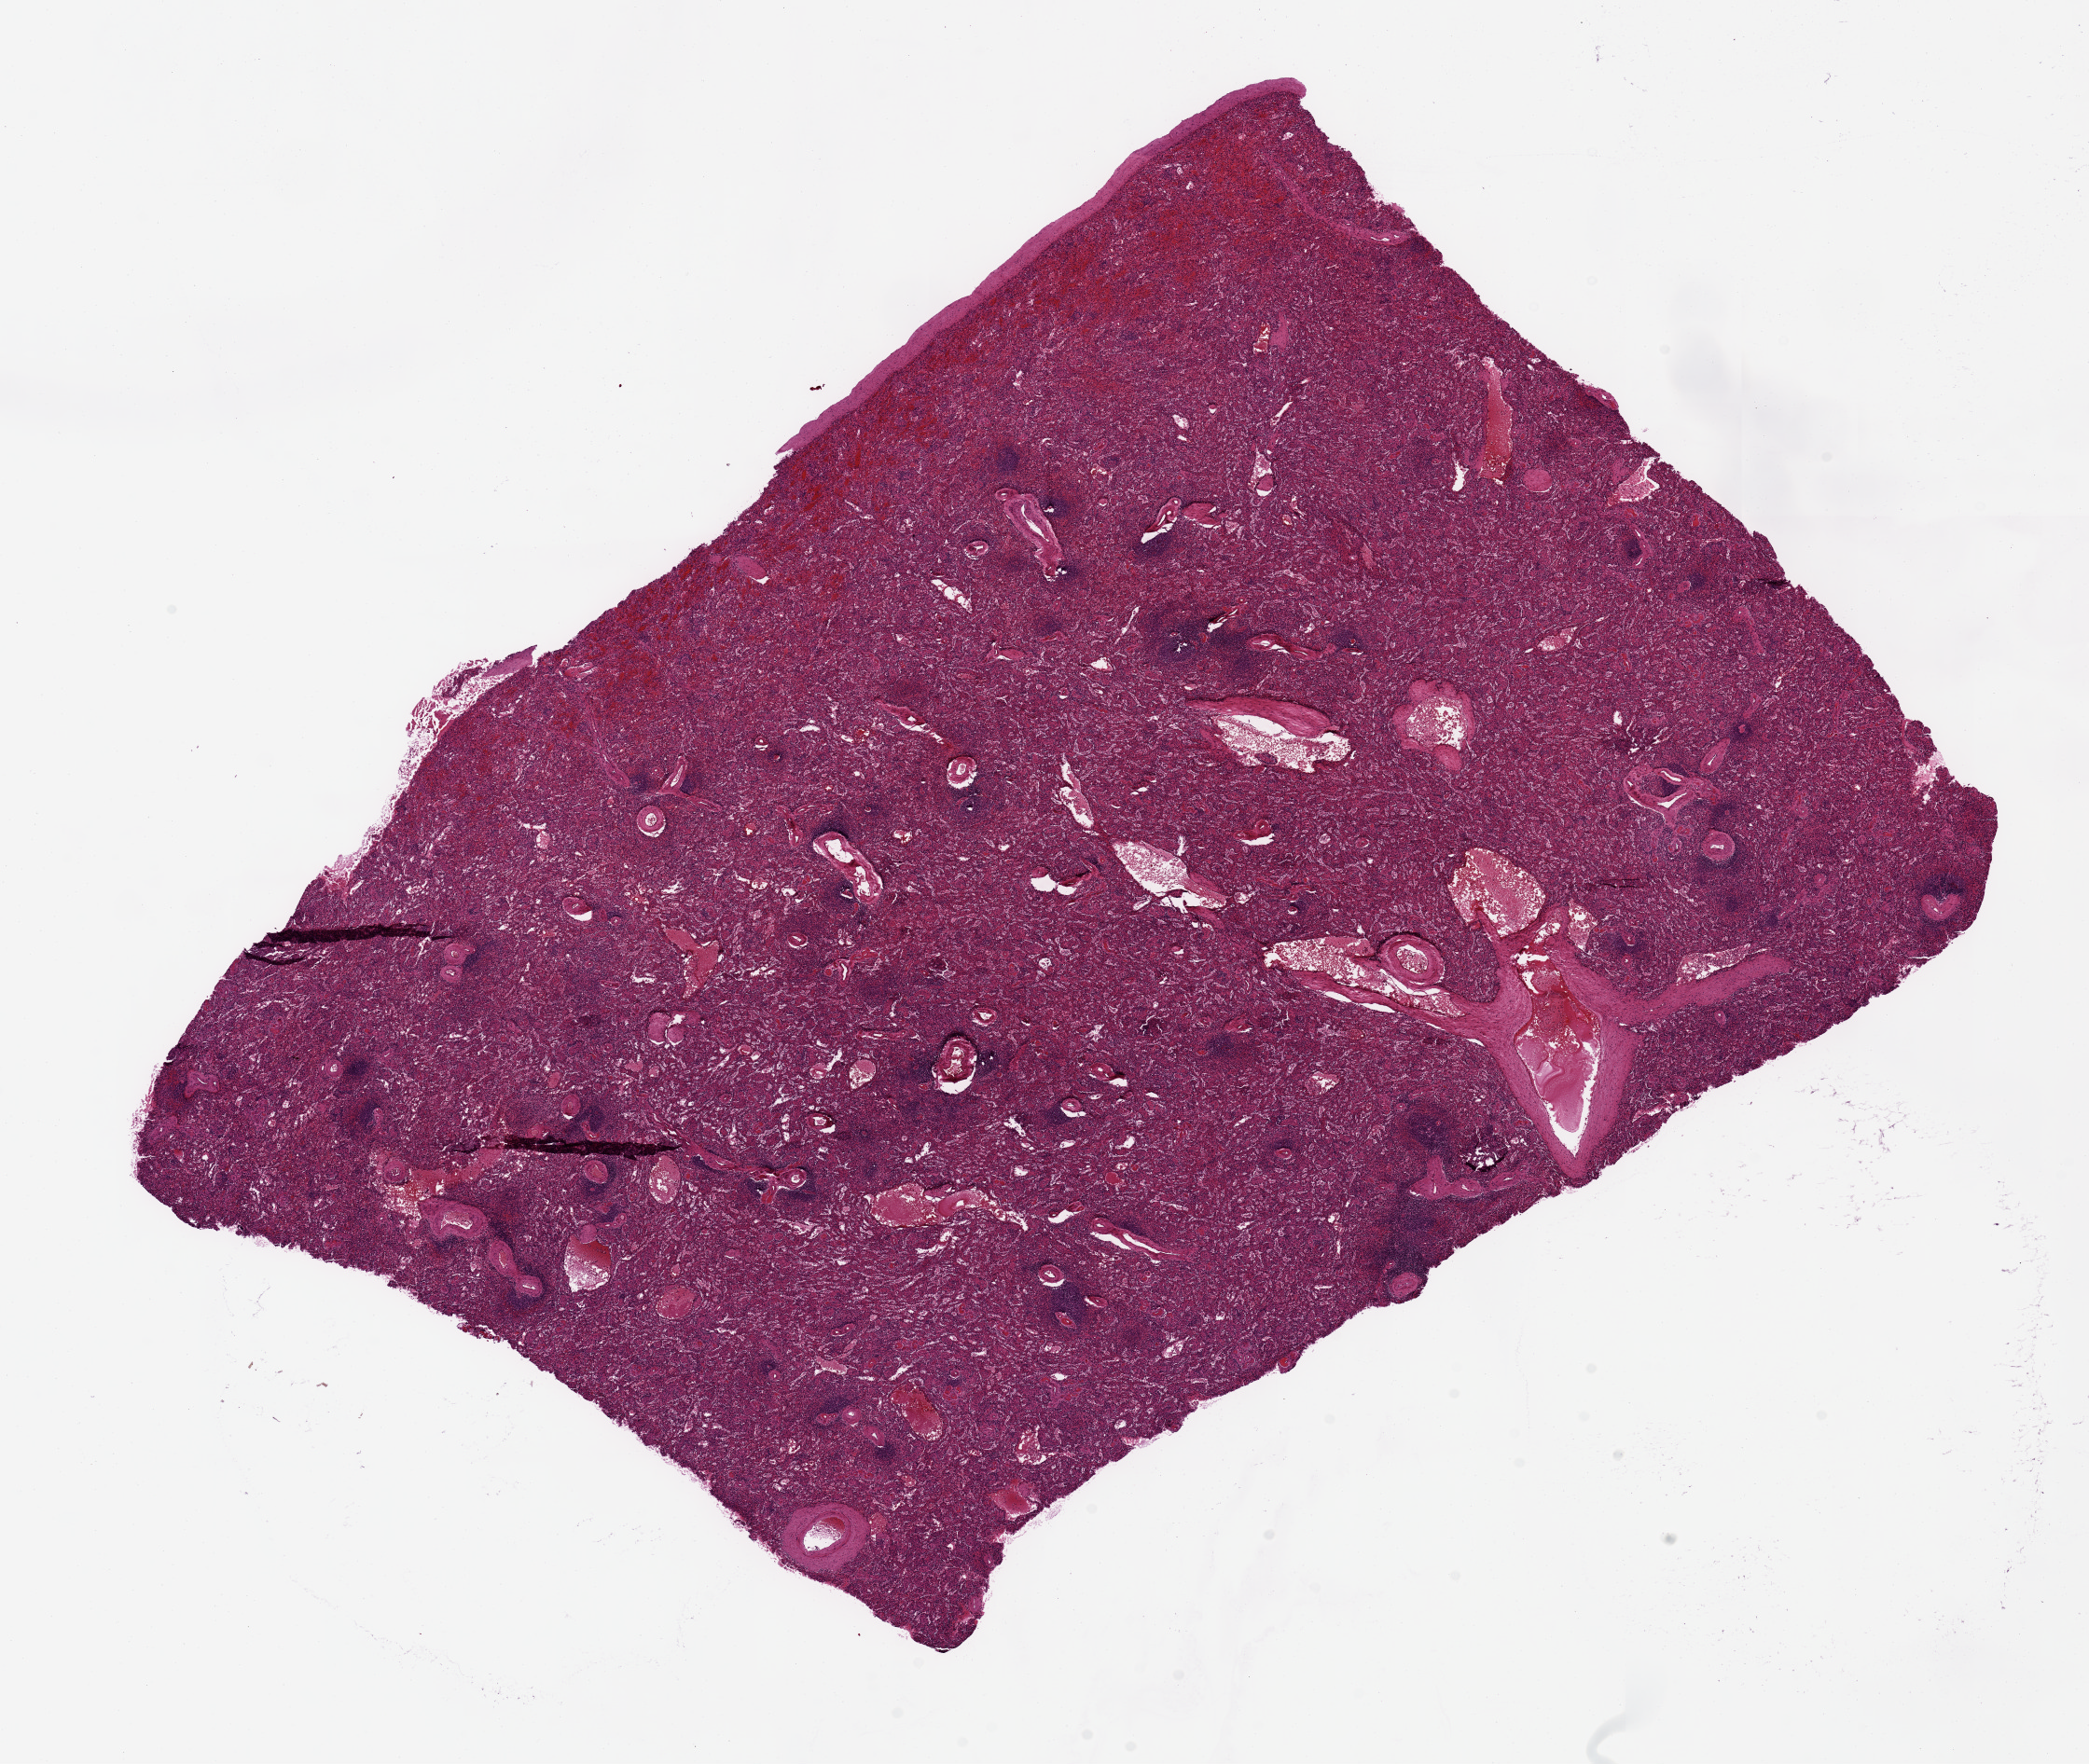
Digitized hematoxylin and eosin (H&E)-stained section — a low-resolution overview of the entire scanned area, about 17.7 x 15.0 mm, PAXgene-fixed, paraffin-embedded tissue, section of spleen (target tissue), tissue donor sample. Male donor.
Pathologist's review note for this sample: 12x9 mm.